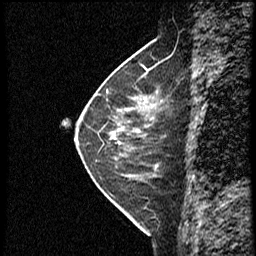
Breast MRI (dynamic contrast-enhanced), one sagittal slice. Position 14 of 40 along the scan axis. Dynamic contrast-enhanced study with each time point stored as its own series, time point 2 of 4 at this slice position (early post-contrast, ordered by acquisition time). 1.5 T. TE 4.2 ms, TR 18.8 ms. 3 mm slice thickness. 256 × 256 image matrix, field of view 200 × 200 mm. Female patient. From the clinical record (not read from this slice): setting: breast cancer imaged before/during neoadjuvant chemotherapy; receptor status: HER2-positive.
Structures marked on this image (semi-automatically segmented with operator editing):
- analysis volume of interest (the breast-tissue region the enhancement analysis was run in; not a lesion): bounding box [x1, y1, x2, y2] px = [91, 79, 163, 153]
- tumour enhancement mask (voxels above the 100 % enhancement threshold inside the analysis volume of interest): [145, 97, 147, 100]